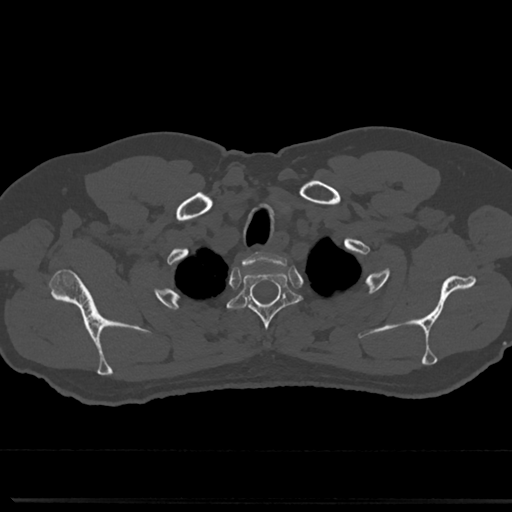
CT including the spine, one axial slice. Slice 639 of 817 in the series (ordered by position). Reconstruction kernel Br40s/3. 120 kVp. Bone window (W 1800 / L 400 HU). 512 × 512 image matrix, field of view 355 × 355 mm. Male patient, age 61 years. Case-level facts recorded for this patient, not image findings: primary cancer: prostate.
Structures marked on this image (semi-automatic segmentation, software-assisted and operator-edited):
- T2 vertebra: box from (x=232, y=263) to (x=296, y=354) px
- T3 vertebra: (x=305, y=315)–(x=309, y=322)